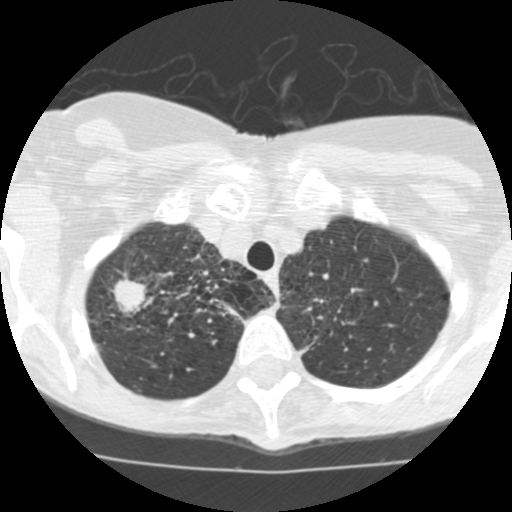
Low-dose screening chest CT, one axial slice; position 97 of 115 along the scan axis; reconstruction kernel STANDARD; 120 kVp; lung window (W 1500 / L -600 HU); 512 × 512 image matrix.
Structures marked on this image (outlined manually by an expert reader):
- lesion 1 (tumor, upper lobe of right lung): bounding box (x1, y1, x2, y2) in pixels: (112, 273, 146, 315)